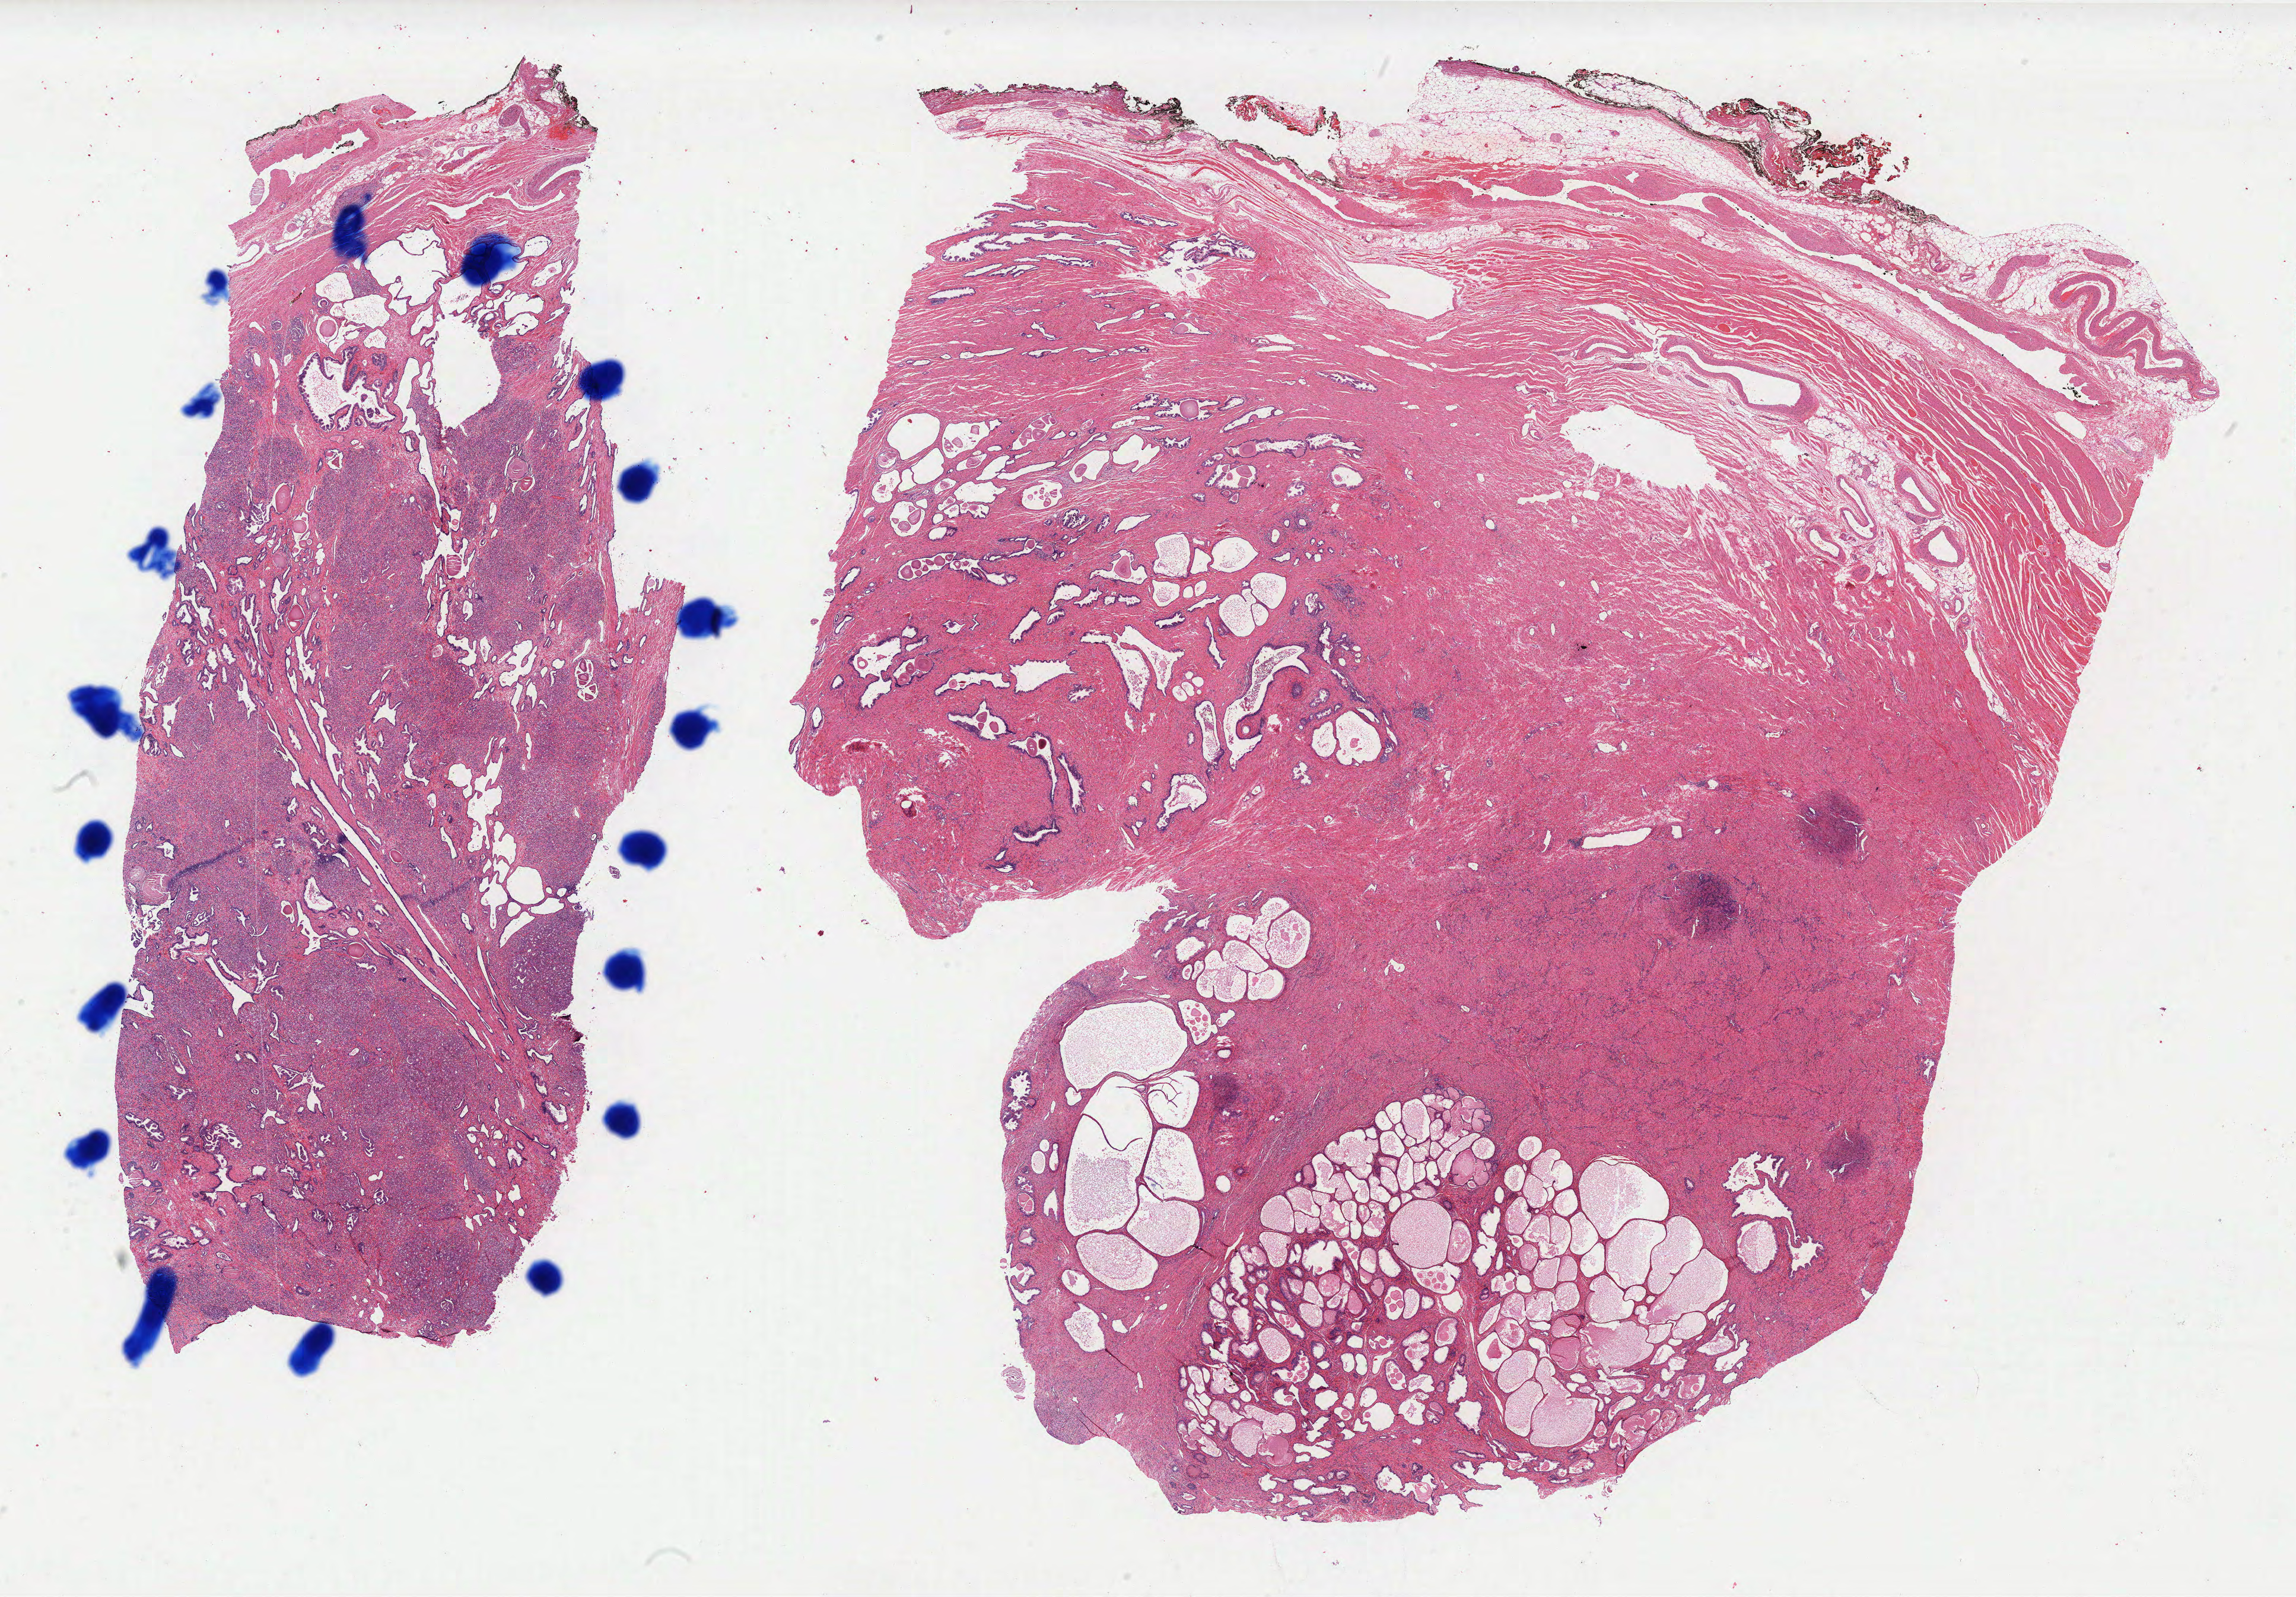
Digitized H&E tissue section (whole slide) — whole scanned area (about 31.0 x 21.5 mm) shown as a low-resolution overview. Formalin-fixed paraffin-embedded (FFPE) diagnostic section. Prostate, primary tumour sample. Male, age 58 years at initial diagnosis.
Pathologic diagnosis: Adenocarcinoma, NOS (prostate gland).